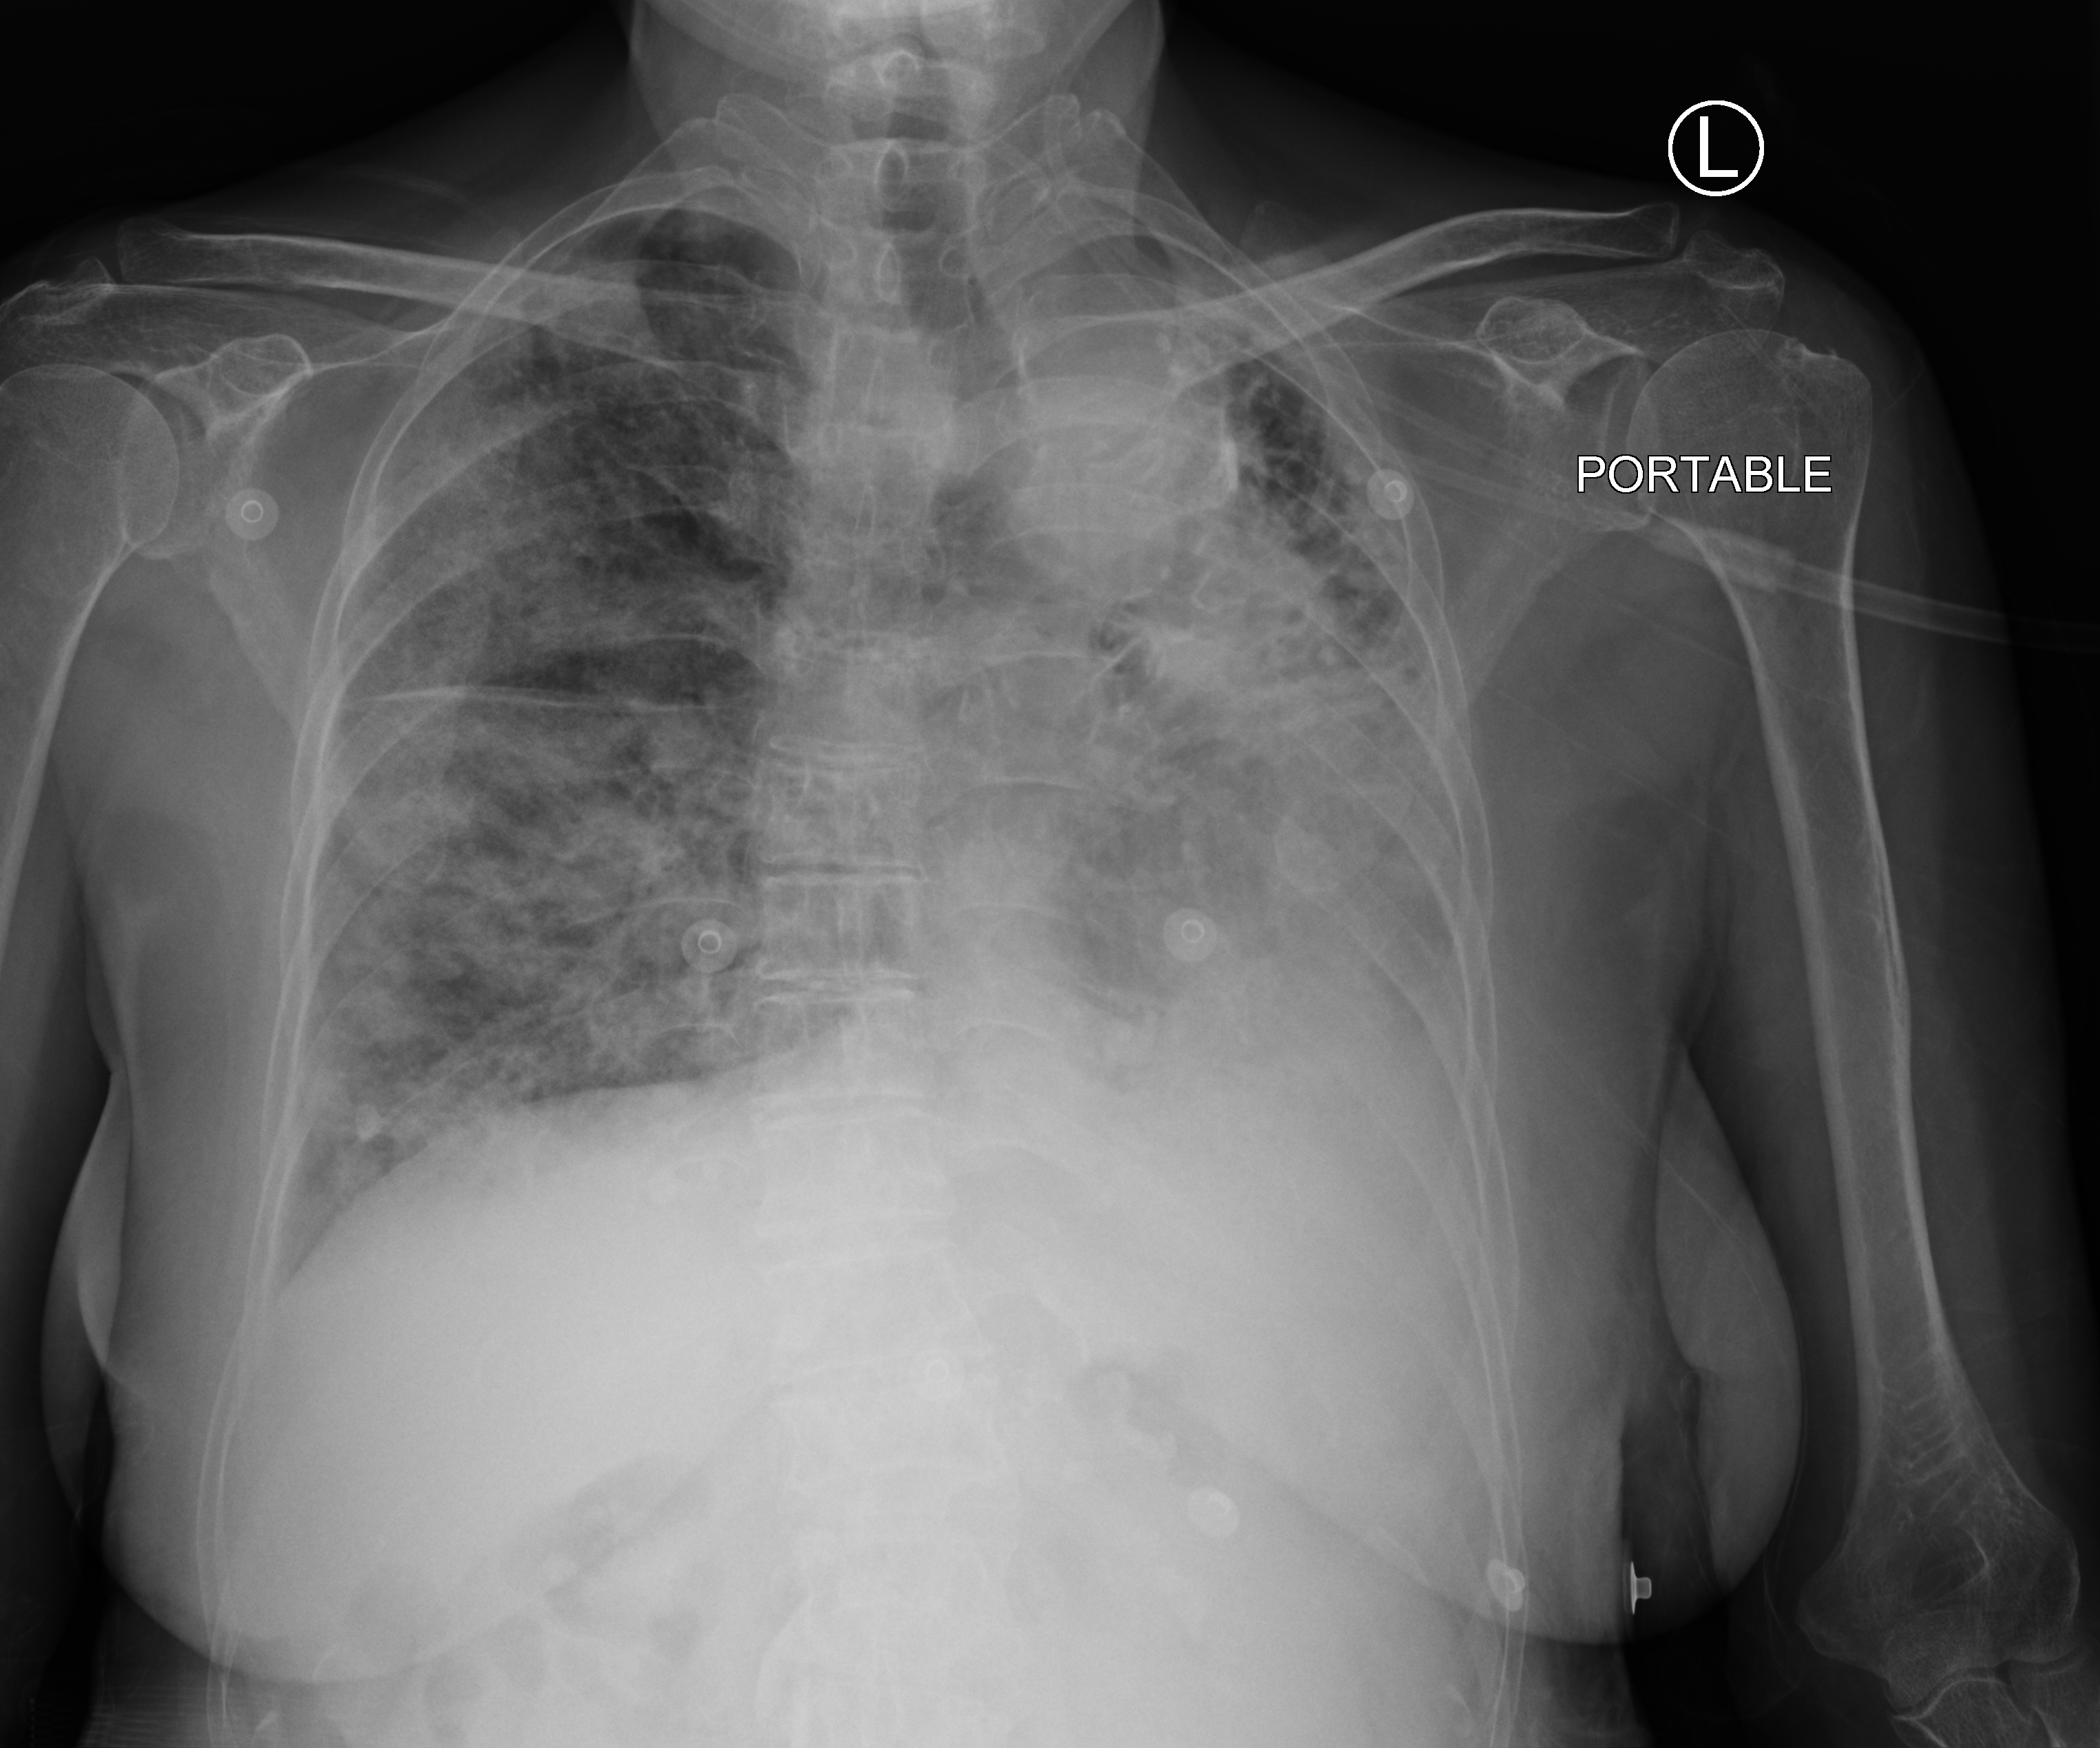
Chest X-ray (portable); anteroposterior (AP) projection. Female patient hospitalised with COVID-19, age 75–90 years.
Admission-level facts for this patient (not findings on this image; timing relative to this image not recorded):
- admitted to intensive care during this hospital stay: no
- mechanically ventilated during this hospital stay: no